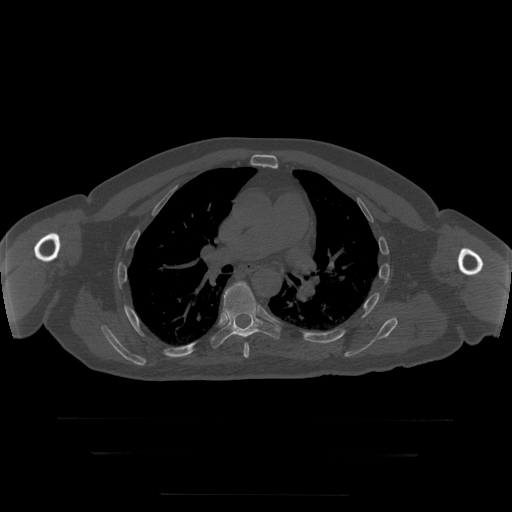
CT including the spine, one axial slice. Position 192 of 397 along the scan axis. Reconstruction kernel STANDARD. Bone window (W 1800 / L 400 HU). 512 × 512 image matrix, field of view 510 × 510 mm. Patient age 73 years. From the clinical record (not read from this slice): primary cancer: prostate.
Outlined on this slice (semi-automatically segmented with operator editing):
- T6 vertebra: bounding box <241,336,249,358> (left, top, right, bottom; pixels)
- T7 vertebra: <211,282,280,348>